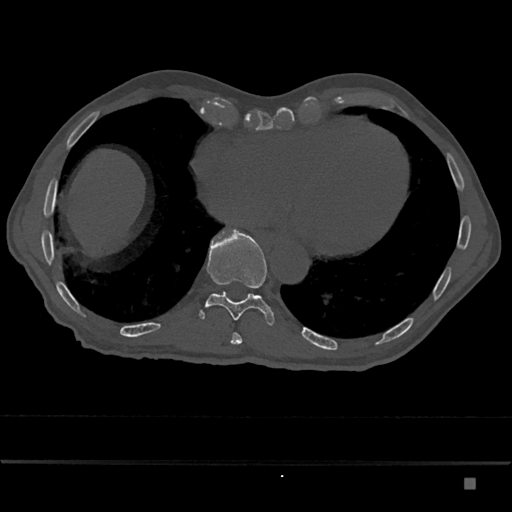
CT including the spine, one axial slice. Position 740 of 797 along the scan axis. Reconstruction kernel Br40s/3. 120 kVp. Bone window (W 1800 / L 400 HU). 512 × 512 image matrix, field of view 390 × 390 mm. Patient: male, 72 years. From the clinical record (not read from this slice): primary cancer: prostate.
Structures marked on this image (semi-automatically segmented with operator editing):
- T10 vertebra: bounding box (x1, y1, x2, y2) in pixels: (199, 230, 274, 325)
- T9 vertebra: (231, 333, 242, 344)